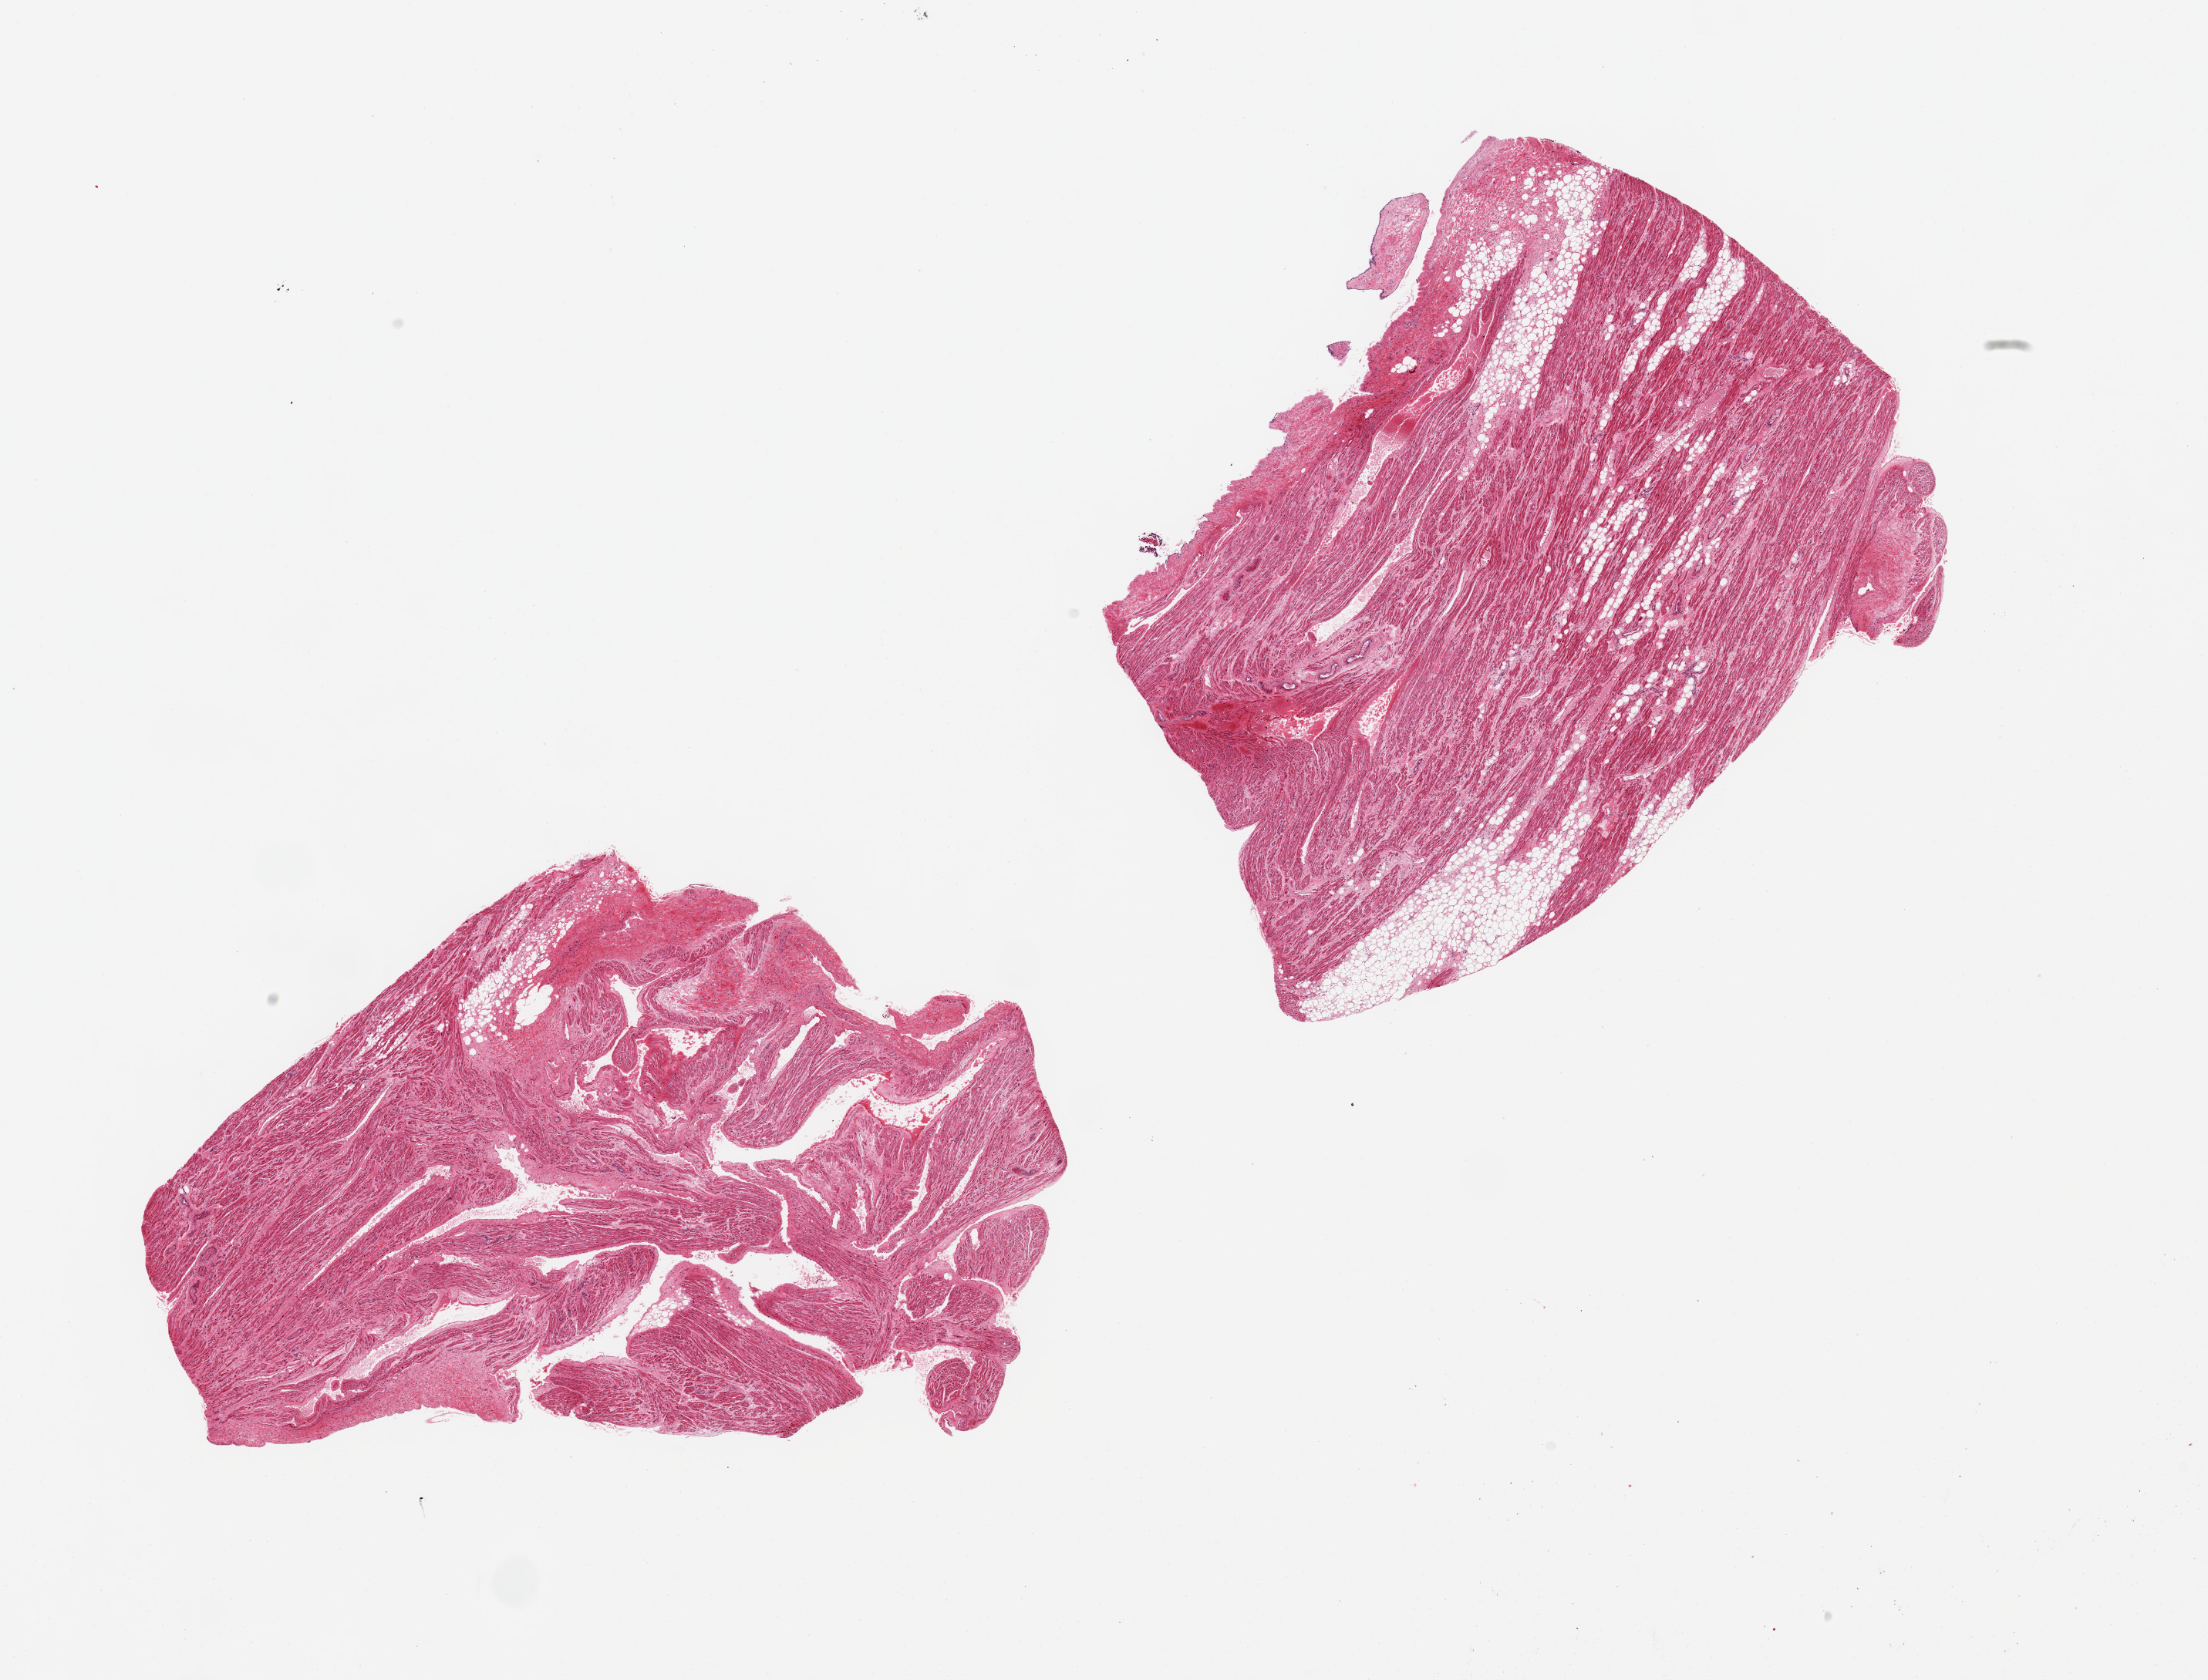
Whole-slide image, haematoxylin and eosin stain, brightfield — whole scanned area (about 22.6 x 17.2 mm) shown as a low-resolution overview; PAXgene-fixed, paraffin-embedded tissue; target tissue: auricular appendage; donor tissue sample. Donor sex: male.
Review note (as recorded): 2 pieces; interstitial fibrosis and one piece with 10-20% internal fat.